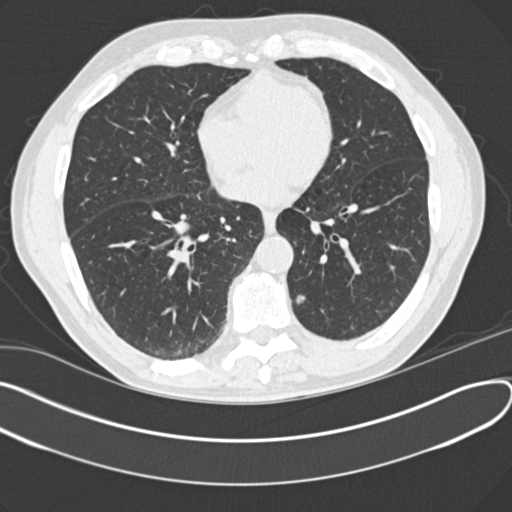
Chest CT (low-dose screening protocol), one axial image; third annual screen; lung window (W 1500 / L -600 HU); 2 mm slice thickness; slice 99 of 166 in the series; 512 × 512 image matrix. Male participant, aged 64 years at enrolment. Former smoker at enrolment.
- Expert reader's lesion annotation, bounding box [x1, y1, x2, y2] px = [282, 281, 324, 319].
- Reader record for this screening exam (exam-level; its link to the box is not recorded): non-calcified nodule or mass ≥4 mm, left lower lobe, 8 × 7 mm, smooth margins, ground glass attenuation.
- Later outcome: lung cancer diagnosed 39 days after this screen — adenocarcinoma with mixed subtypes, left lower lobe, well differentiated (G1), stage IA (AJCC 6th edition), 7 mm at pathology.